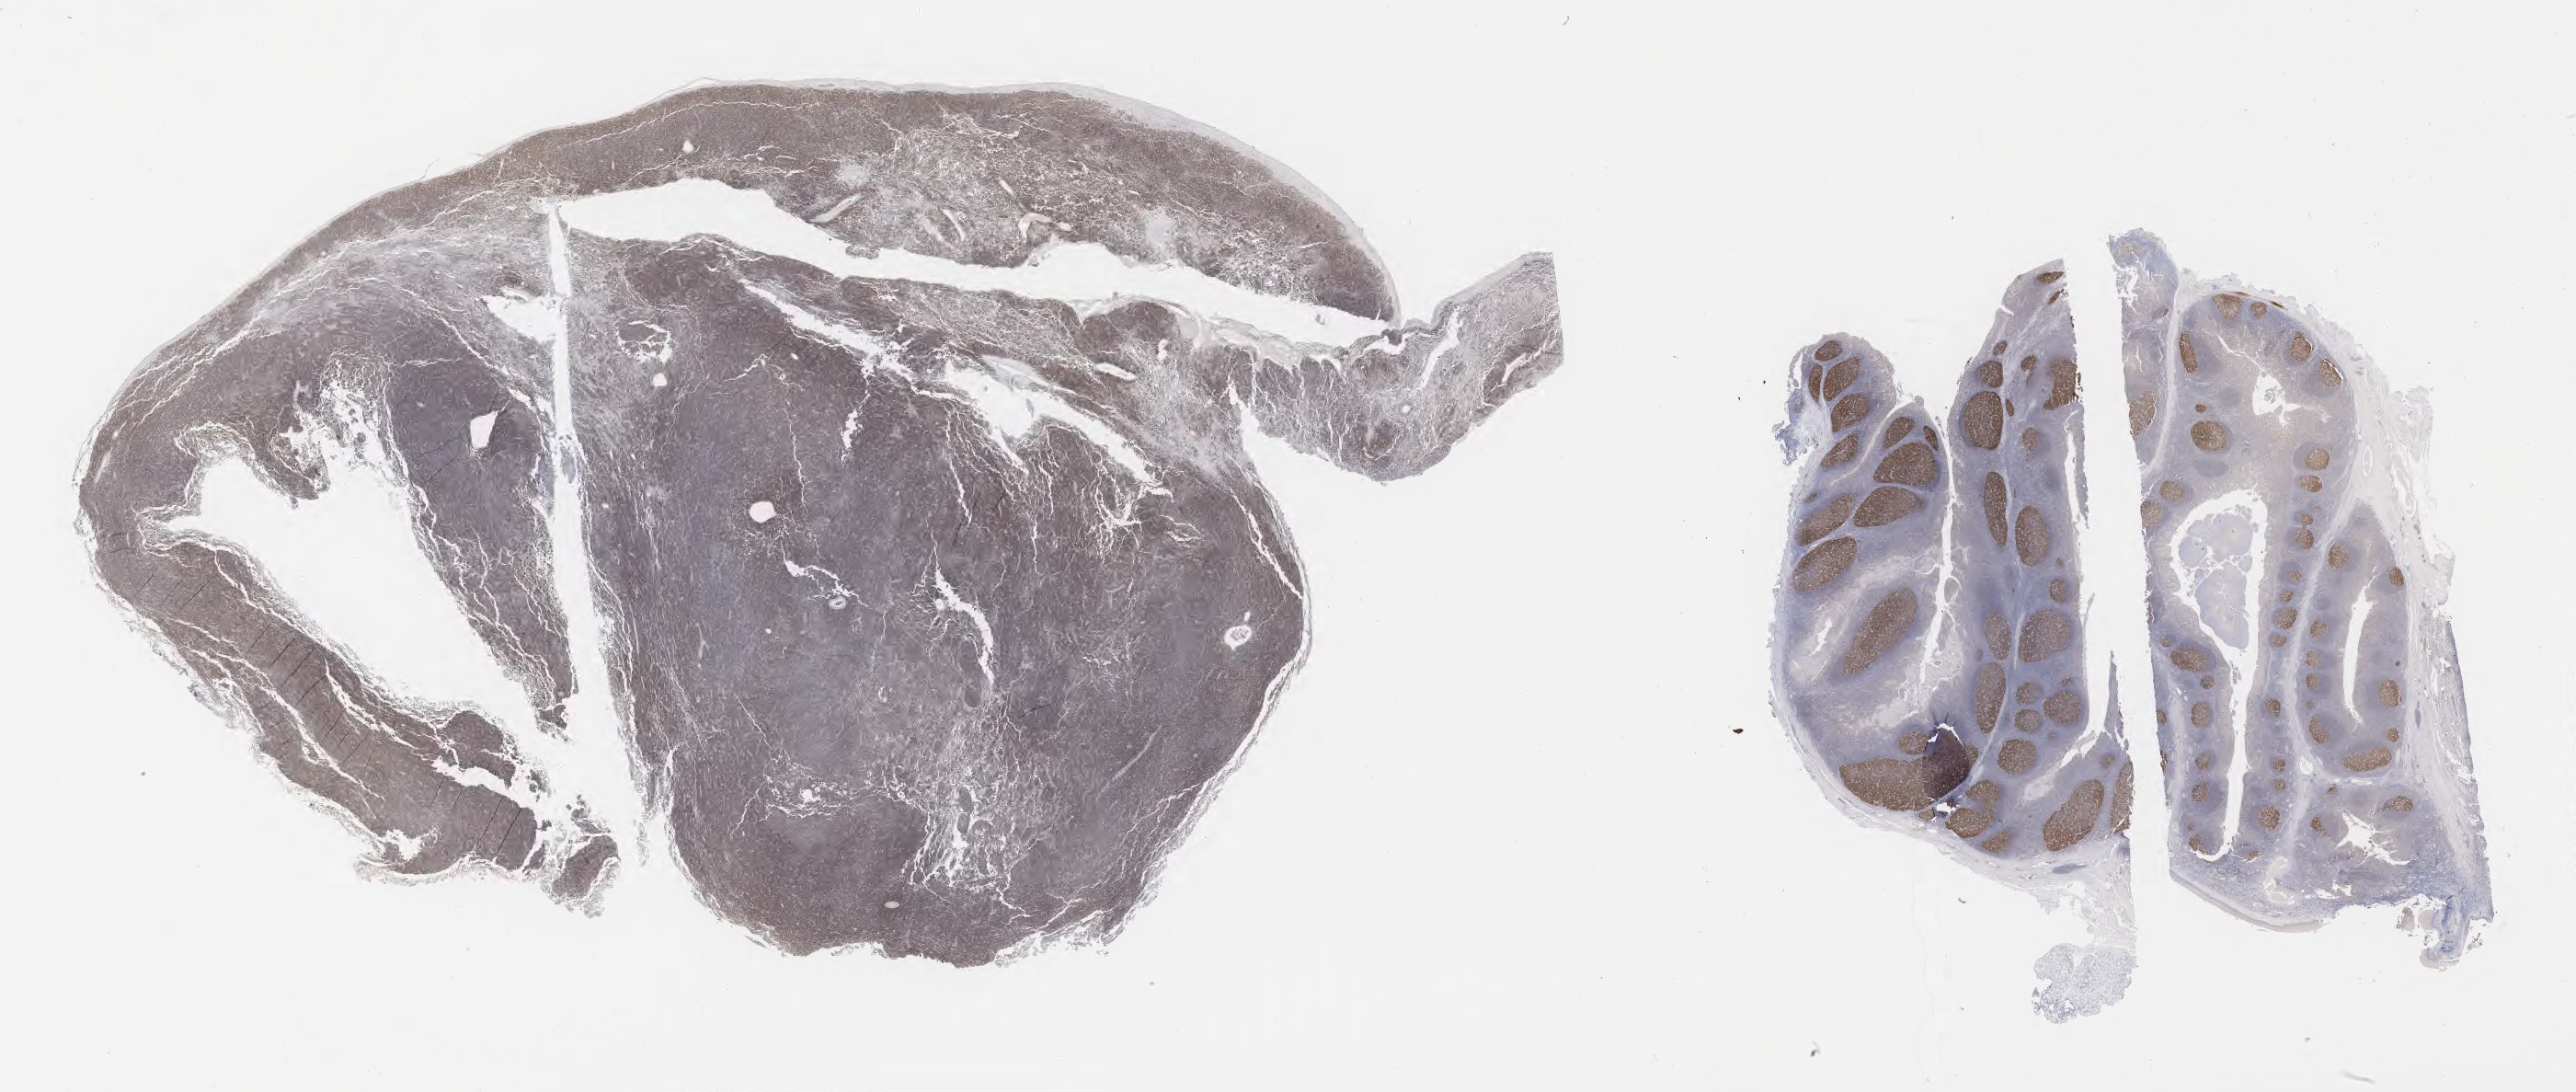
IHC for BCL6, whole-slide image — a low-resolution overview of the entire scanned area, about 45.3 x 19.2 mm, specimen: tumor tissue. Patient: female, age at initial diagnosis 3 years.
Histologic diagnosis: Burkitt lymphoma, NOS.